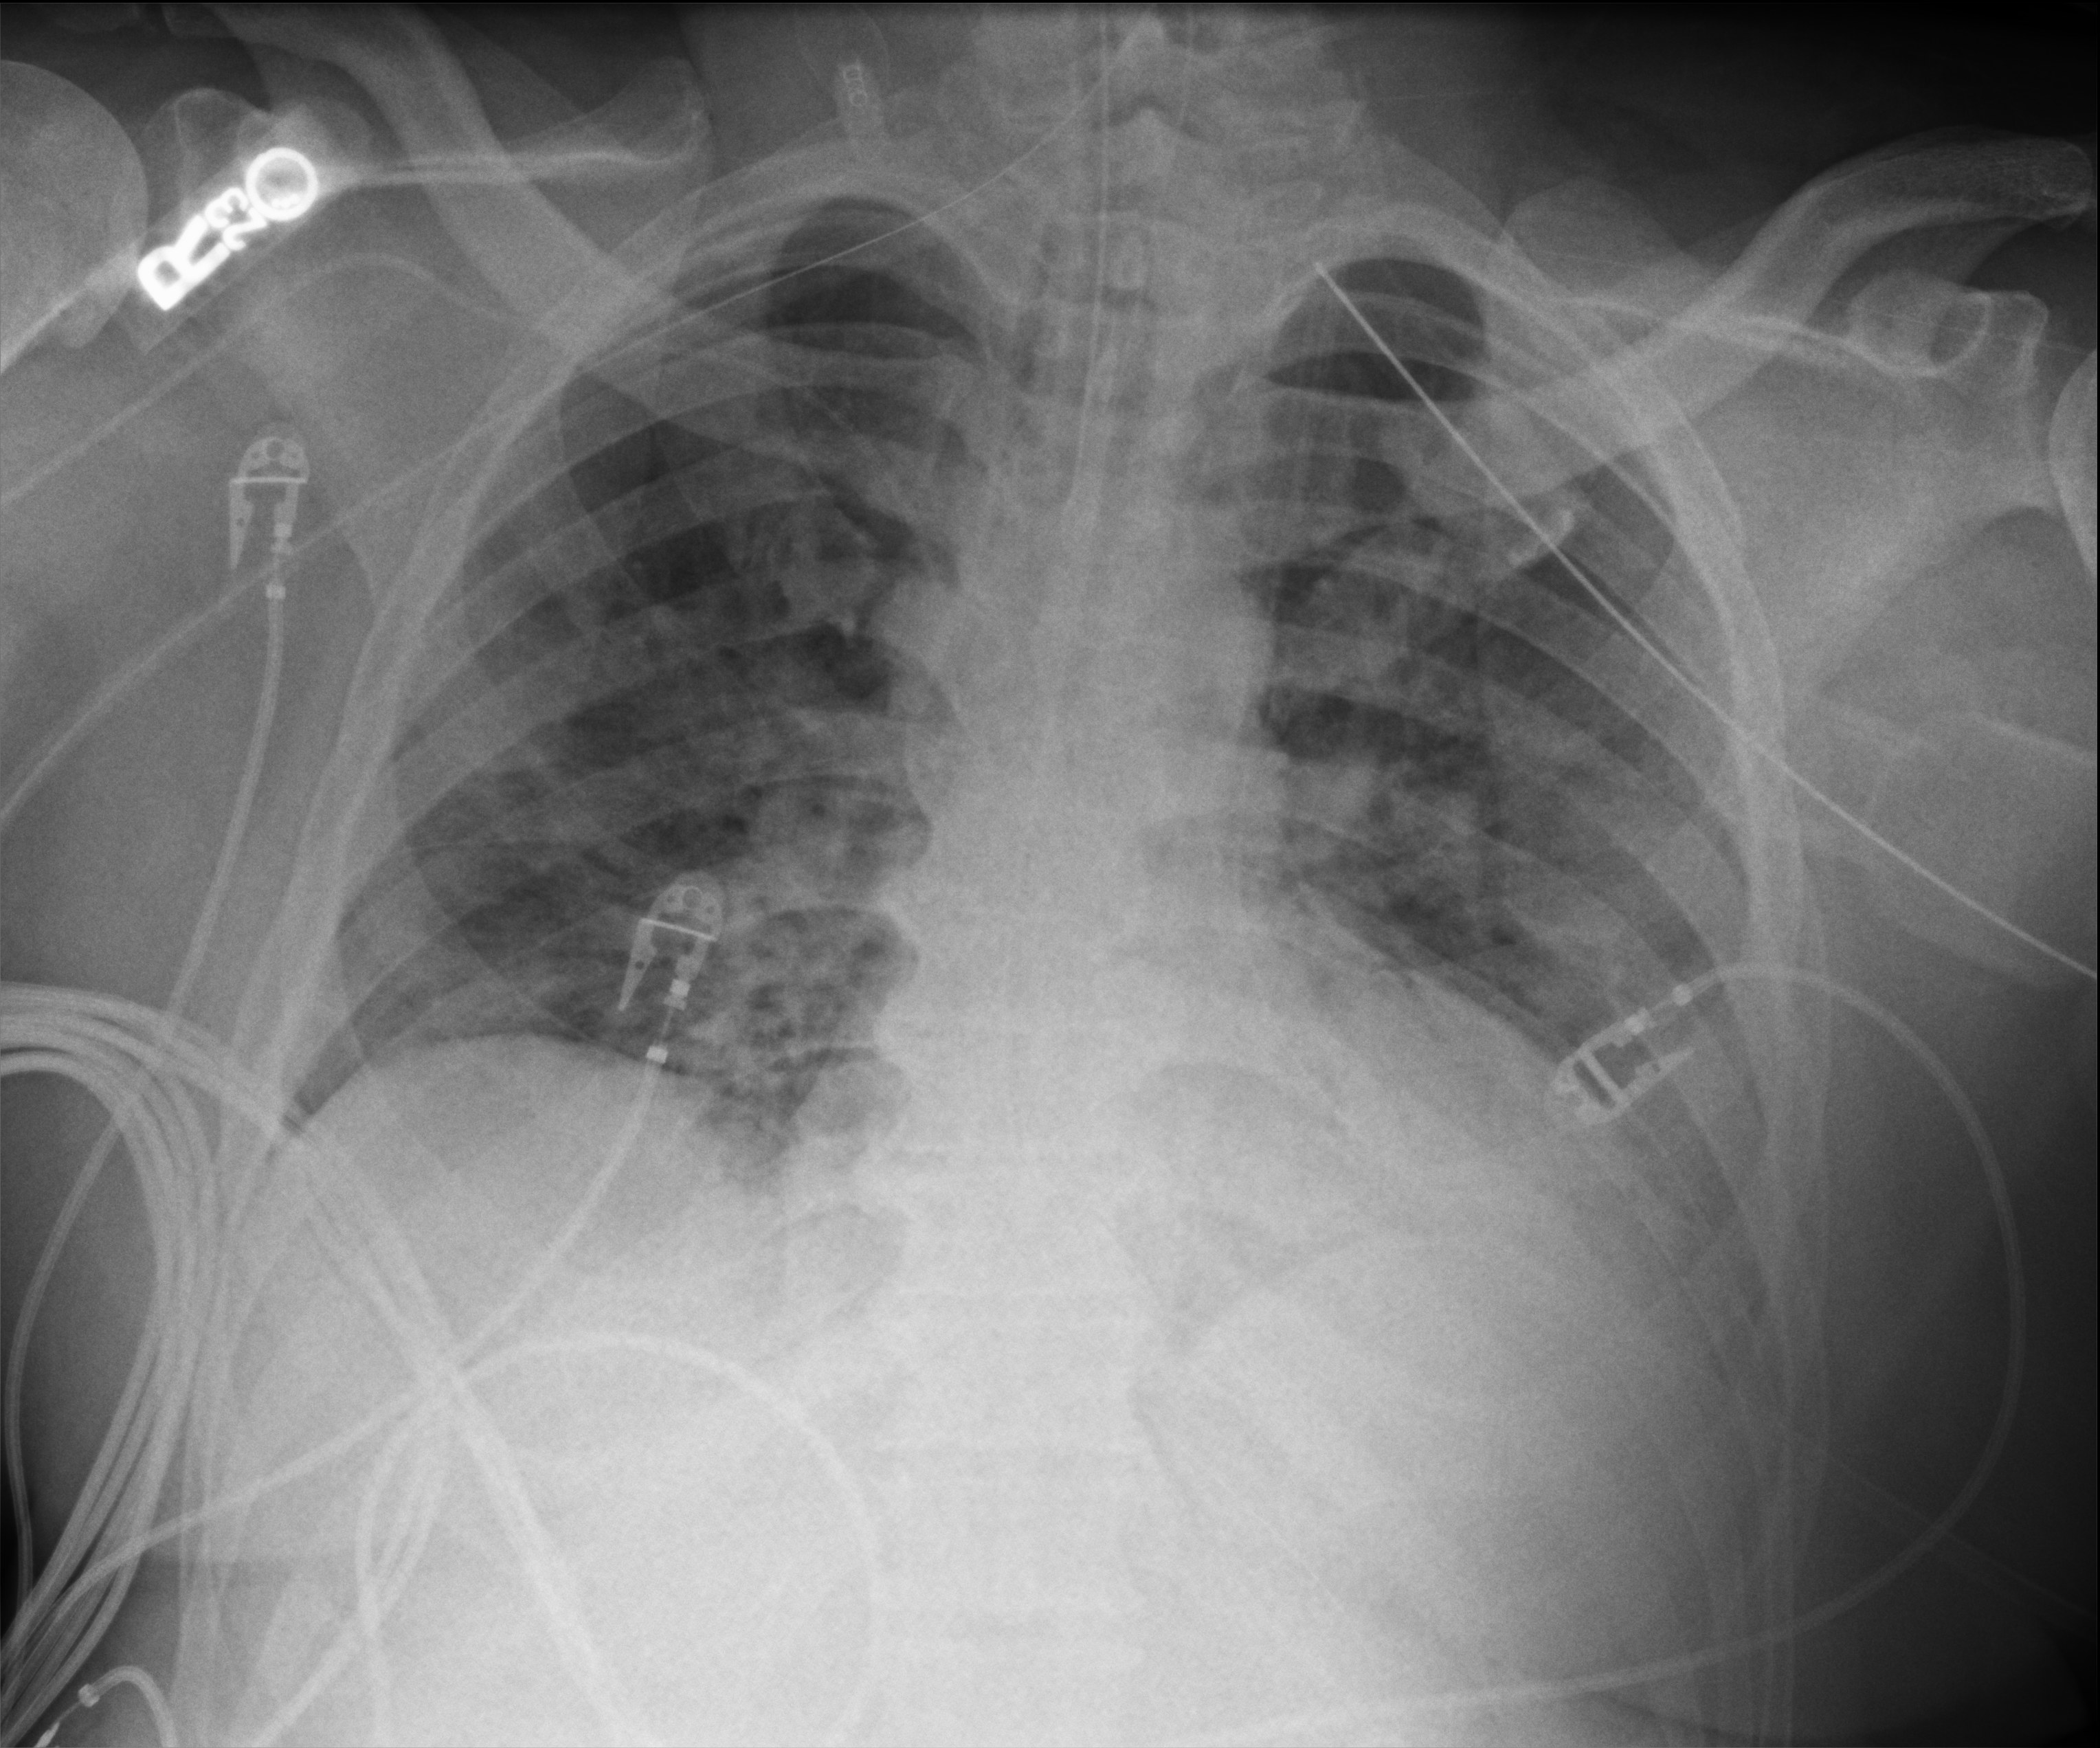
Portable chest radiograph; anteroposterior (AP) projection. Male patient hospitalised with COVID-19, age 18–59 years.
Admission-level facts for this patient (not findings on this image; timing relative to this image not recorded):
- admitted to intensive care during this hospital stay: yes